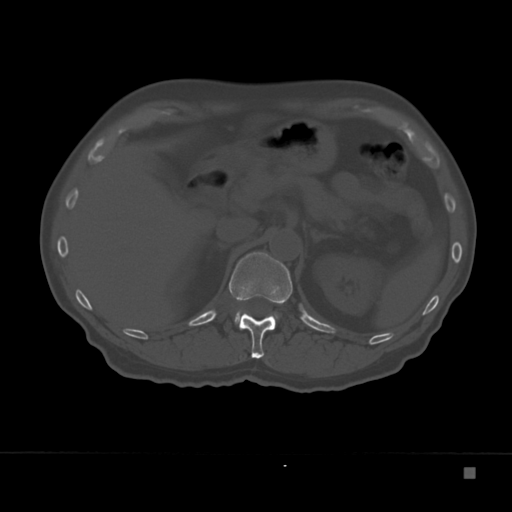
CT including the spine, one axial slice. Slice 127 of 332 in the series (ordered by position). 120 kVp. Bone window (W 1800 / L 400 HU). 512 × 512 image matrix, field of view 389 × 389 mm. Patient: male, 72 years. Case-level facts recorded for this patient, not image findings: primary cancer: skeletal.
Annotated regions visible in this slice (semi-automatically segmented with operator editing):
- L1 vertebra: bounding box <234,311,278,327> (left, top, right, bottom; pixels)
- T12 vertebra: <229,252,293,359>